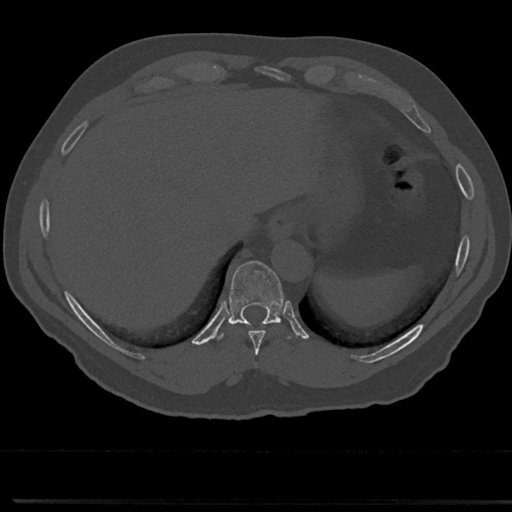
CT including the spine, one axial slice. Reconstruction kernel Br40s/3. 120 kVp. Bone window (W 1800 / L 400 HU). 0.5 mm slice thickness. 512 × 512 image matrix, field of view 355 × 355 mm. Male patient, age 61 years. From the clinical record (not read from this slice): primary cancer: prostate.
Structures marked on this image (semi-automatic segmentation, software-assisted and operator-edited):
- T10 vertebra: box from (x=230, y=262) to (x=281, y=323) px
- T8 vertebra: (x=237, y=319)–(x=280, y=370)
- T9 vertebra: (x=228, y=284)–(x=287, y=348)